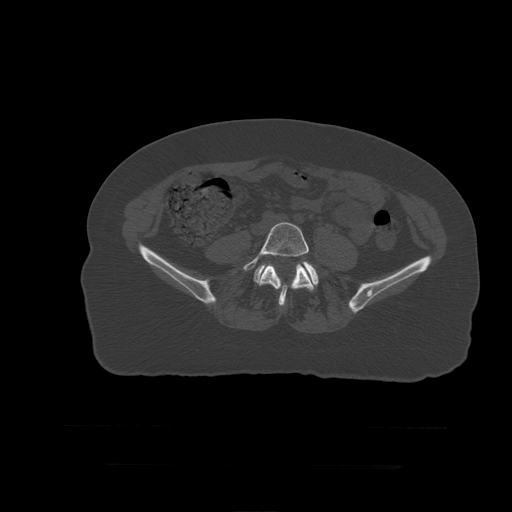
CT including the spine, one axial slice; position 70 of 399 along the scan axis; reconstruction kernel STANDARD; bone window (W 1800 / L 400 HU); 1.25 mm slice thickness; 512 × 512 image matrix, field of view 450 × 450 mm. Patient age 41 years. Case-level facts recorded for this patient, not image findings: primary cancer: breast.
Structures marked on this image (semi-automatic segmentation, software-assisted and operator-edited):
- L5 vertebra: bounding box (x1, y1, x2, y2) in pixels: (243, 223, 315, 307)